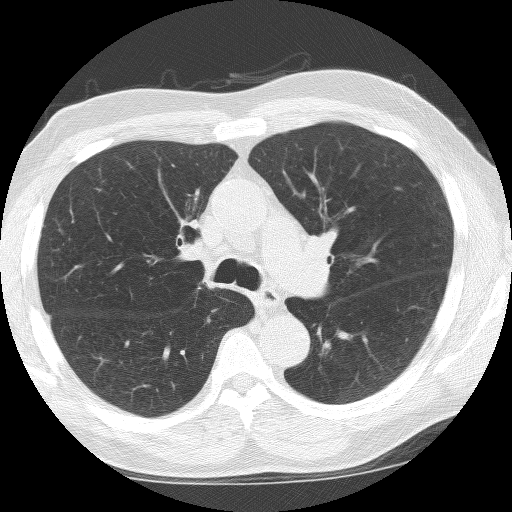
Low-dose screening chest CT, one axial slice. Slice 96 of 155 in the series (ordered by position). Reconstruction kernel BONE. Lung window (W 1500 / L -600 HU). 512 × 512 image matrix, field of view 323 × 323 mm.
Outlined on this slice (outlined manually by an expert reader):
- lesion 1 (tumor, lower lobe of left lung): bounding box [x1, y1, x2, y2] px = [319, 338, 331, 355]